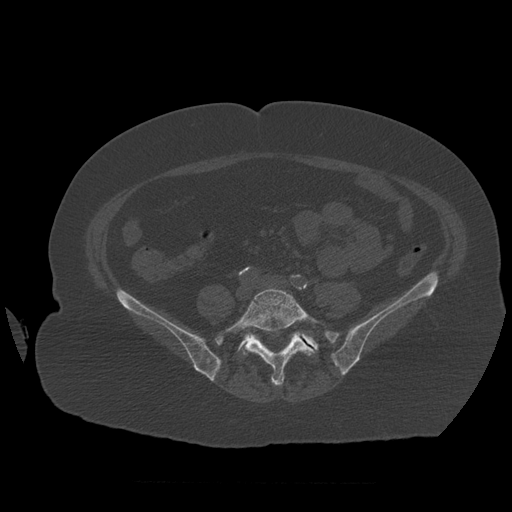
CT including the spine, one axial slice; position 181 of 399 along the scan axis; 120 kVp; bone window (W 1800 / L 400 HU); 1.25 mm slice thickness; 512 × 512 image matrix, field of view 404 × 404 mm. Patient age 81 years. Case-level facts recorded for this patient, not image findings: primary cancer: renal; vertebrae with lytic lesions (as recorded): L1.
Structures marked on this image (semi-automatic segmentation, software-assisted and operator-edited):
- L5 vertebra: bounding box [x1, y1, x2, y2] px = [221, 288, 319, 386]